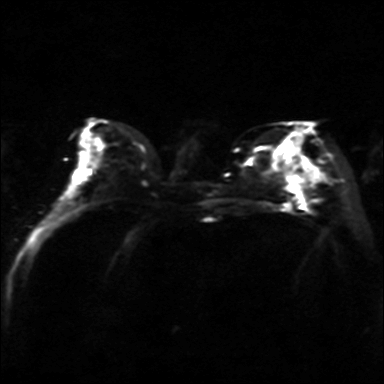
Breast MRI, one axial slice. Slice 18 of 36 in the series (ordered by position). Diffusion-weighted series; image 2 of 4 stored at this slice position (different b-values; order by instance number). 3 T. 4 mm slice thickness. 384 × 384 image matrix. Female patient.
Outlined on this slice (manually delineated by an expert):
- tumour on diffusion-weighted imaging: bounding box [x1, y1, x2, y2] px = [289, 176, 302, 190]